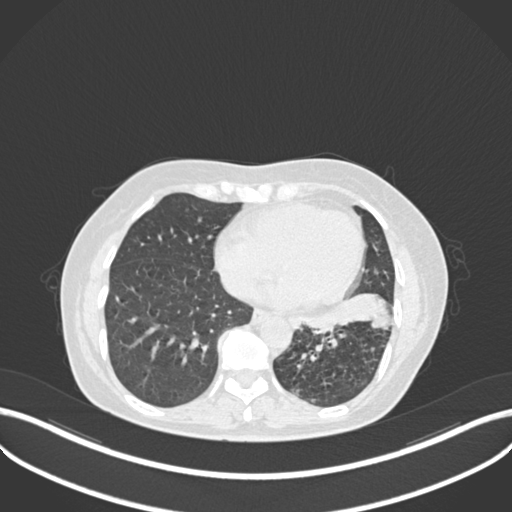
Chest CT, one axial slice. Slice 93 of 270 in the series (ordered by position). Reconstruction kernel B30f. 120 kVp. Lung window (W 1500 / L -600 HU). 1 mm slice thickness. 512 × 512 image matrix, field of view 400 × 400 mm. Female patient, age 63 years. From the clinical record (not read from this slice): clinical TNM (as recorded): T1b N0 M0.
Annotated regions visible in this slice (bounding box drawn by a radiologist):
- lung tumour (recorded histology: adenocarcinoma): bounding box (x1, y1, x2, y2) in pixels: (304, 294, 398, 334)